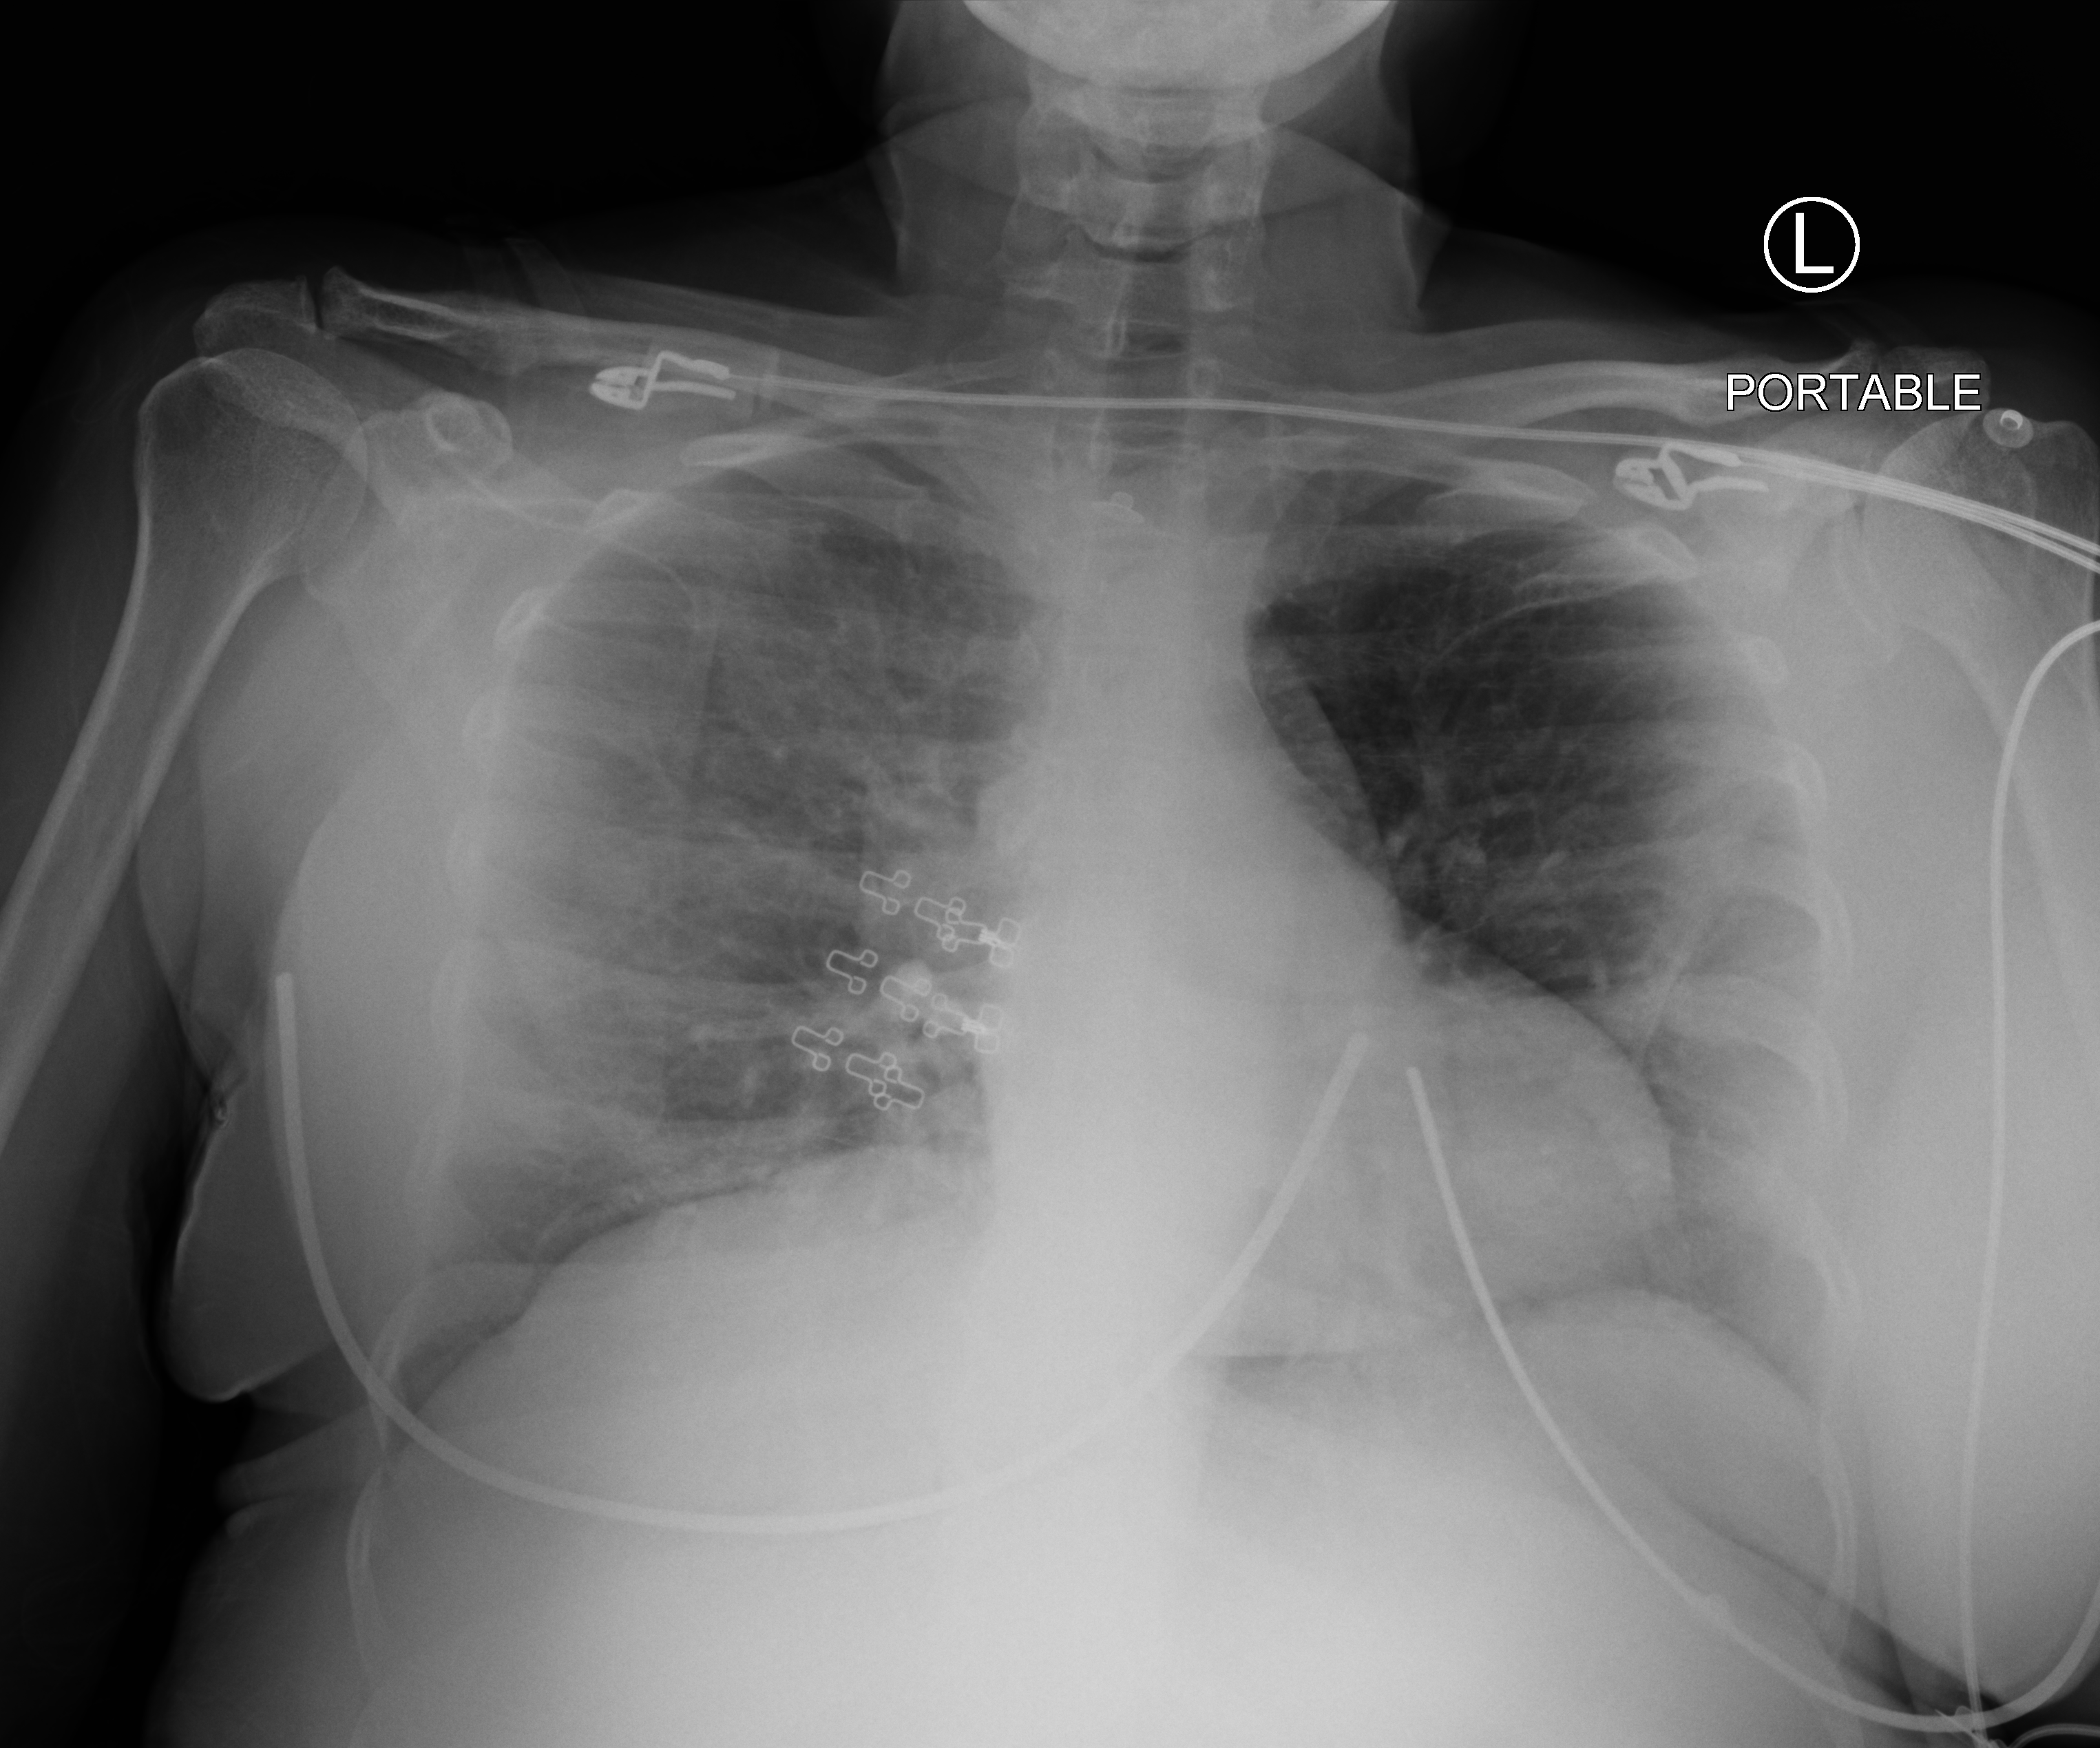
Portable chest radiograph, anteroposterior (AP) projection. Patient hospitalised with COVID-19; female, aged 18–59 years.
Admission-level facts for this patient (not findings on this image; timing relative to this image not recorded): length of hospital stay: 8 days; mechanically ventilated during this hospital stay: no.